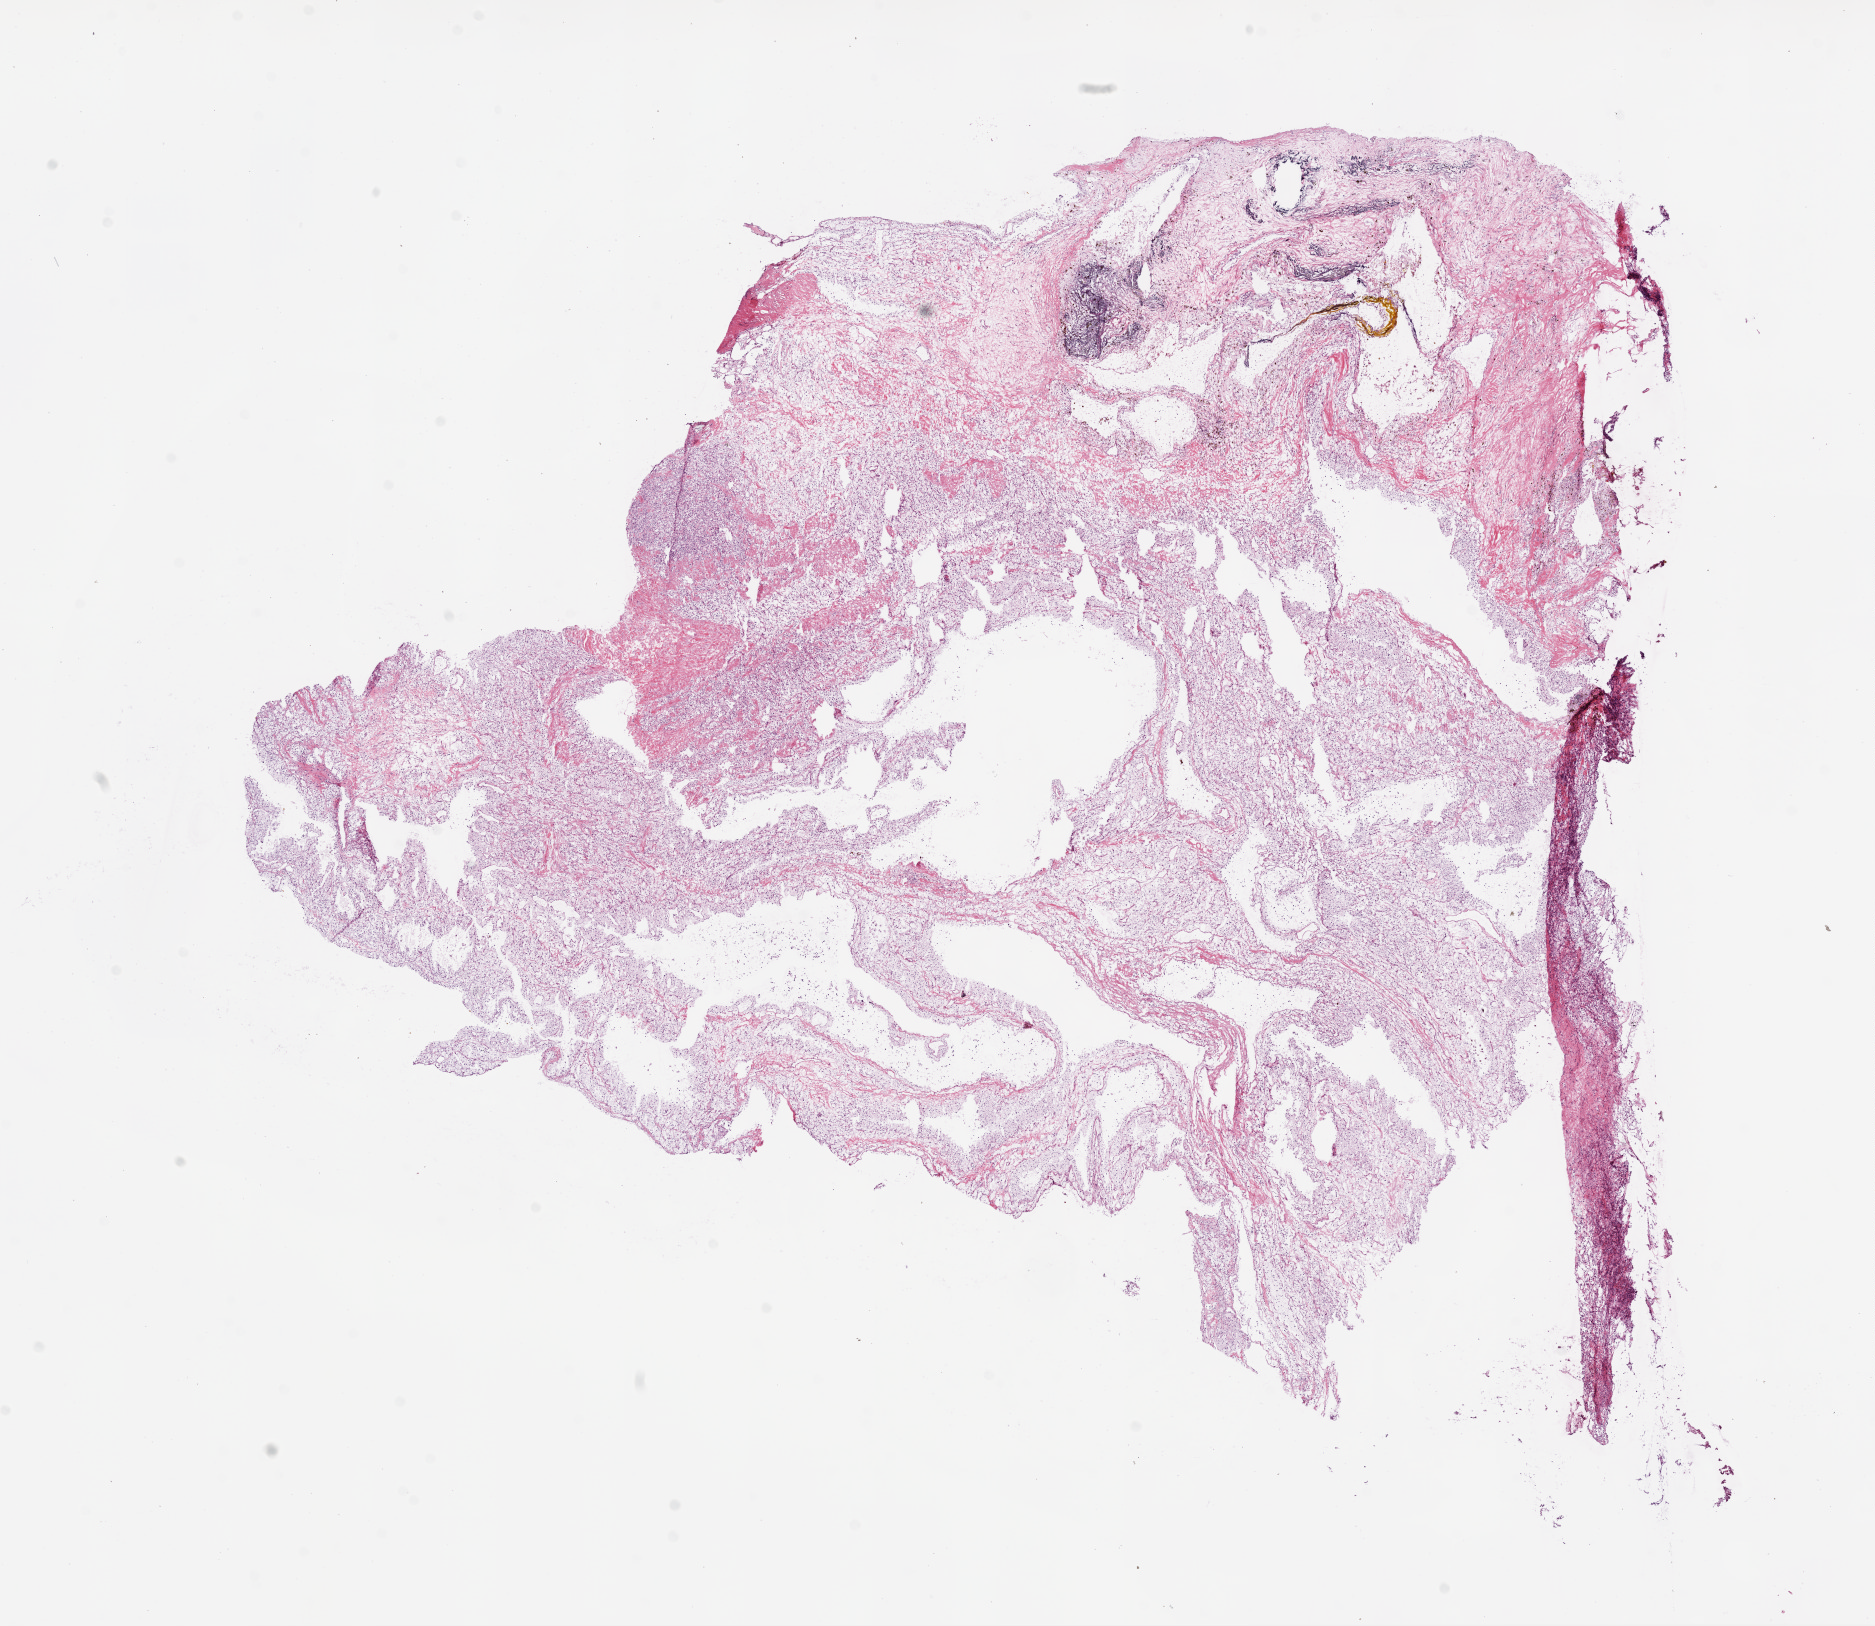
Digitized Hematoxylin and eosin (H&E) stained tissue section (whole slide), shown as a low-resolution overview of the whole scanned area (about 15.0 x 13.0 mm). Frozen section from the bottom of the tissue portion. Kidney, primary tumour sample. Patient: female, age at initial diagnosis 43 years. Histologic grade: G3 (poorly differentiated). Slide review estimates, as recorded: tumour cells 80%, tumour nuclei 80%, normal cells 0%, stromal cells 20%, necrosis 0%.
- AJCC pathologic stage: III
- histologic diagnosis: Clear cell adenocarcinoma, NOS